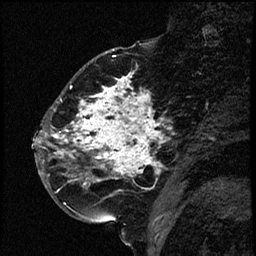
Breast MRI (dynamic contrast-enhanced), one sagittal slice. Position 26 of 66 along the scan axis. Dynamic contrast-enhanced study with each time point stored as its own series, time point 2 of 3 at this slice position (early post-contrast, ordered by acquisition time). 1.5 T. TE 4.2 ms, TR 17.6 ms. 2 mm slice thickness. 256 × 256 image matrix, field of view 200 × 200 mm. Female patient. From the clinical record (not read from this slice): setting: breast cancer imaged before/during neoadjuvant chemotherapy; receptor status: HER2-positive.
Annotated regions visible in this slice (semi-automatically segmented with operator editing):
- analysis volume of interest (the breast-tissue region the enhancement analysis was run in; not a lesion): bounding box [x1, y1, x2, y2] px = [52, 69, 174, 209]
- tumour enhancement mask (voxels above the 100 % enhancement threshold inside the analysis volume of interest): [52, 74, 160, 187]